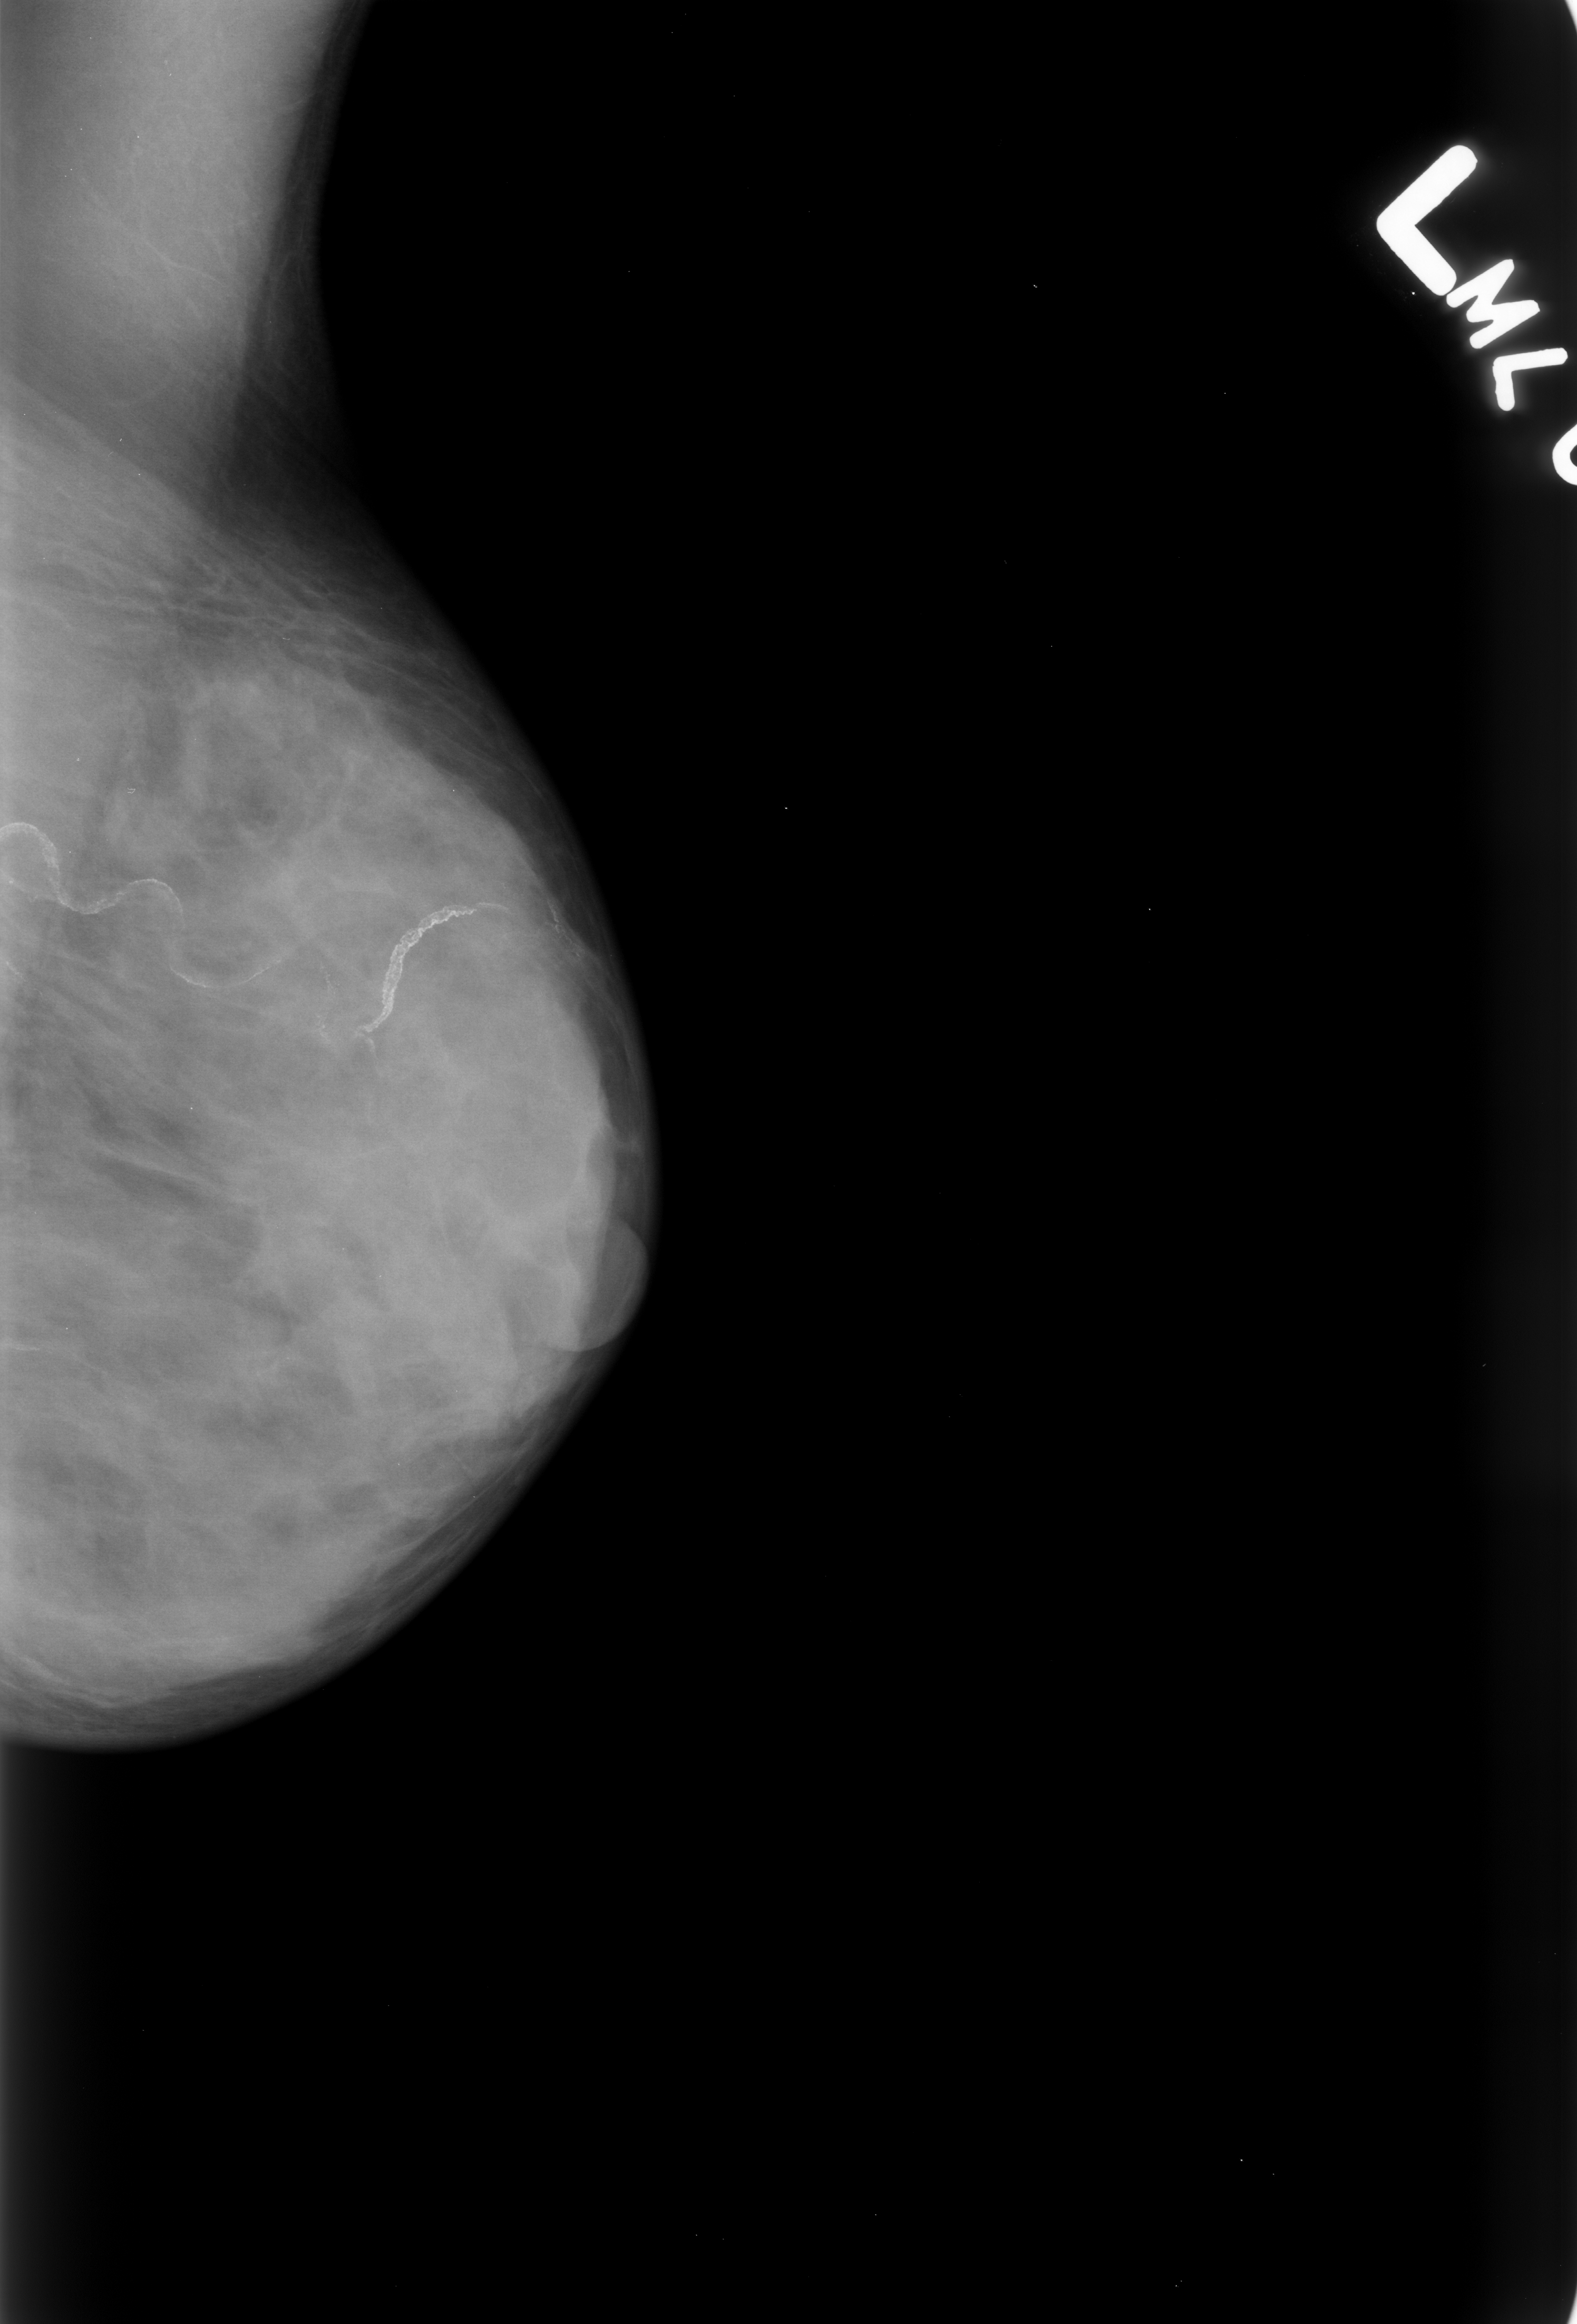
Digitized screen-film mammogram. Left breast. MLO view. BI-RADS breast density category 4 (scale 1–4). 1577 × 2324 image matrix.
Expert-marked regions of interest on this image (one box per marked abnormality):
- calcifications, morphology vascular; BI-RADS assessment category 2; subtlety rating 5 on a 1 (subtle) to 5 (obvious) scale; outcome (as recorded, no biopsy): benign without callback (not worked up further): bounding box <0,797,296,1013> (left, top, right, bottom; pixels)